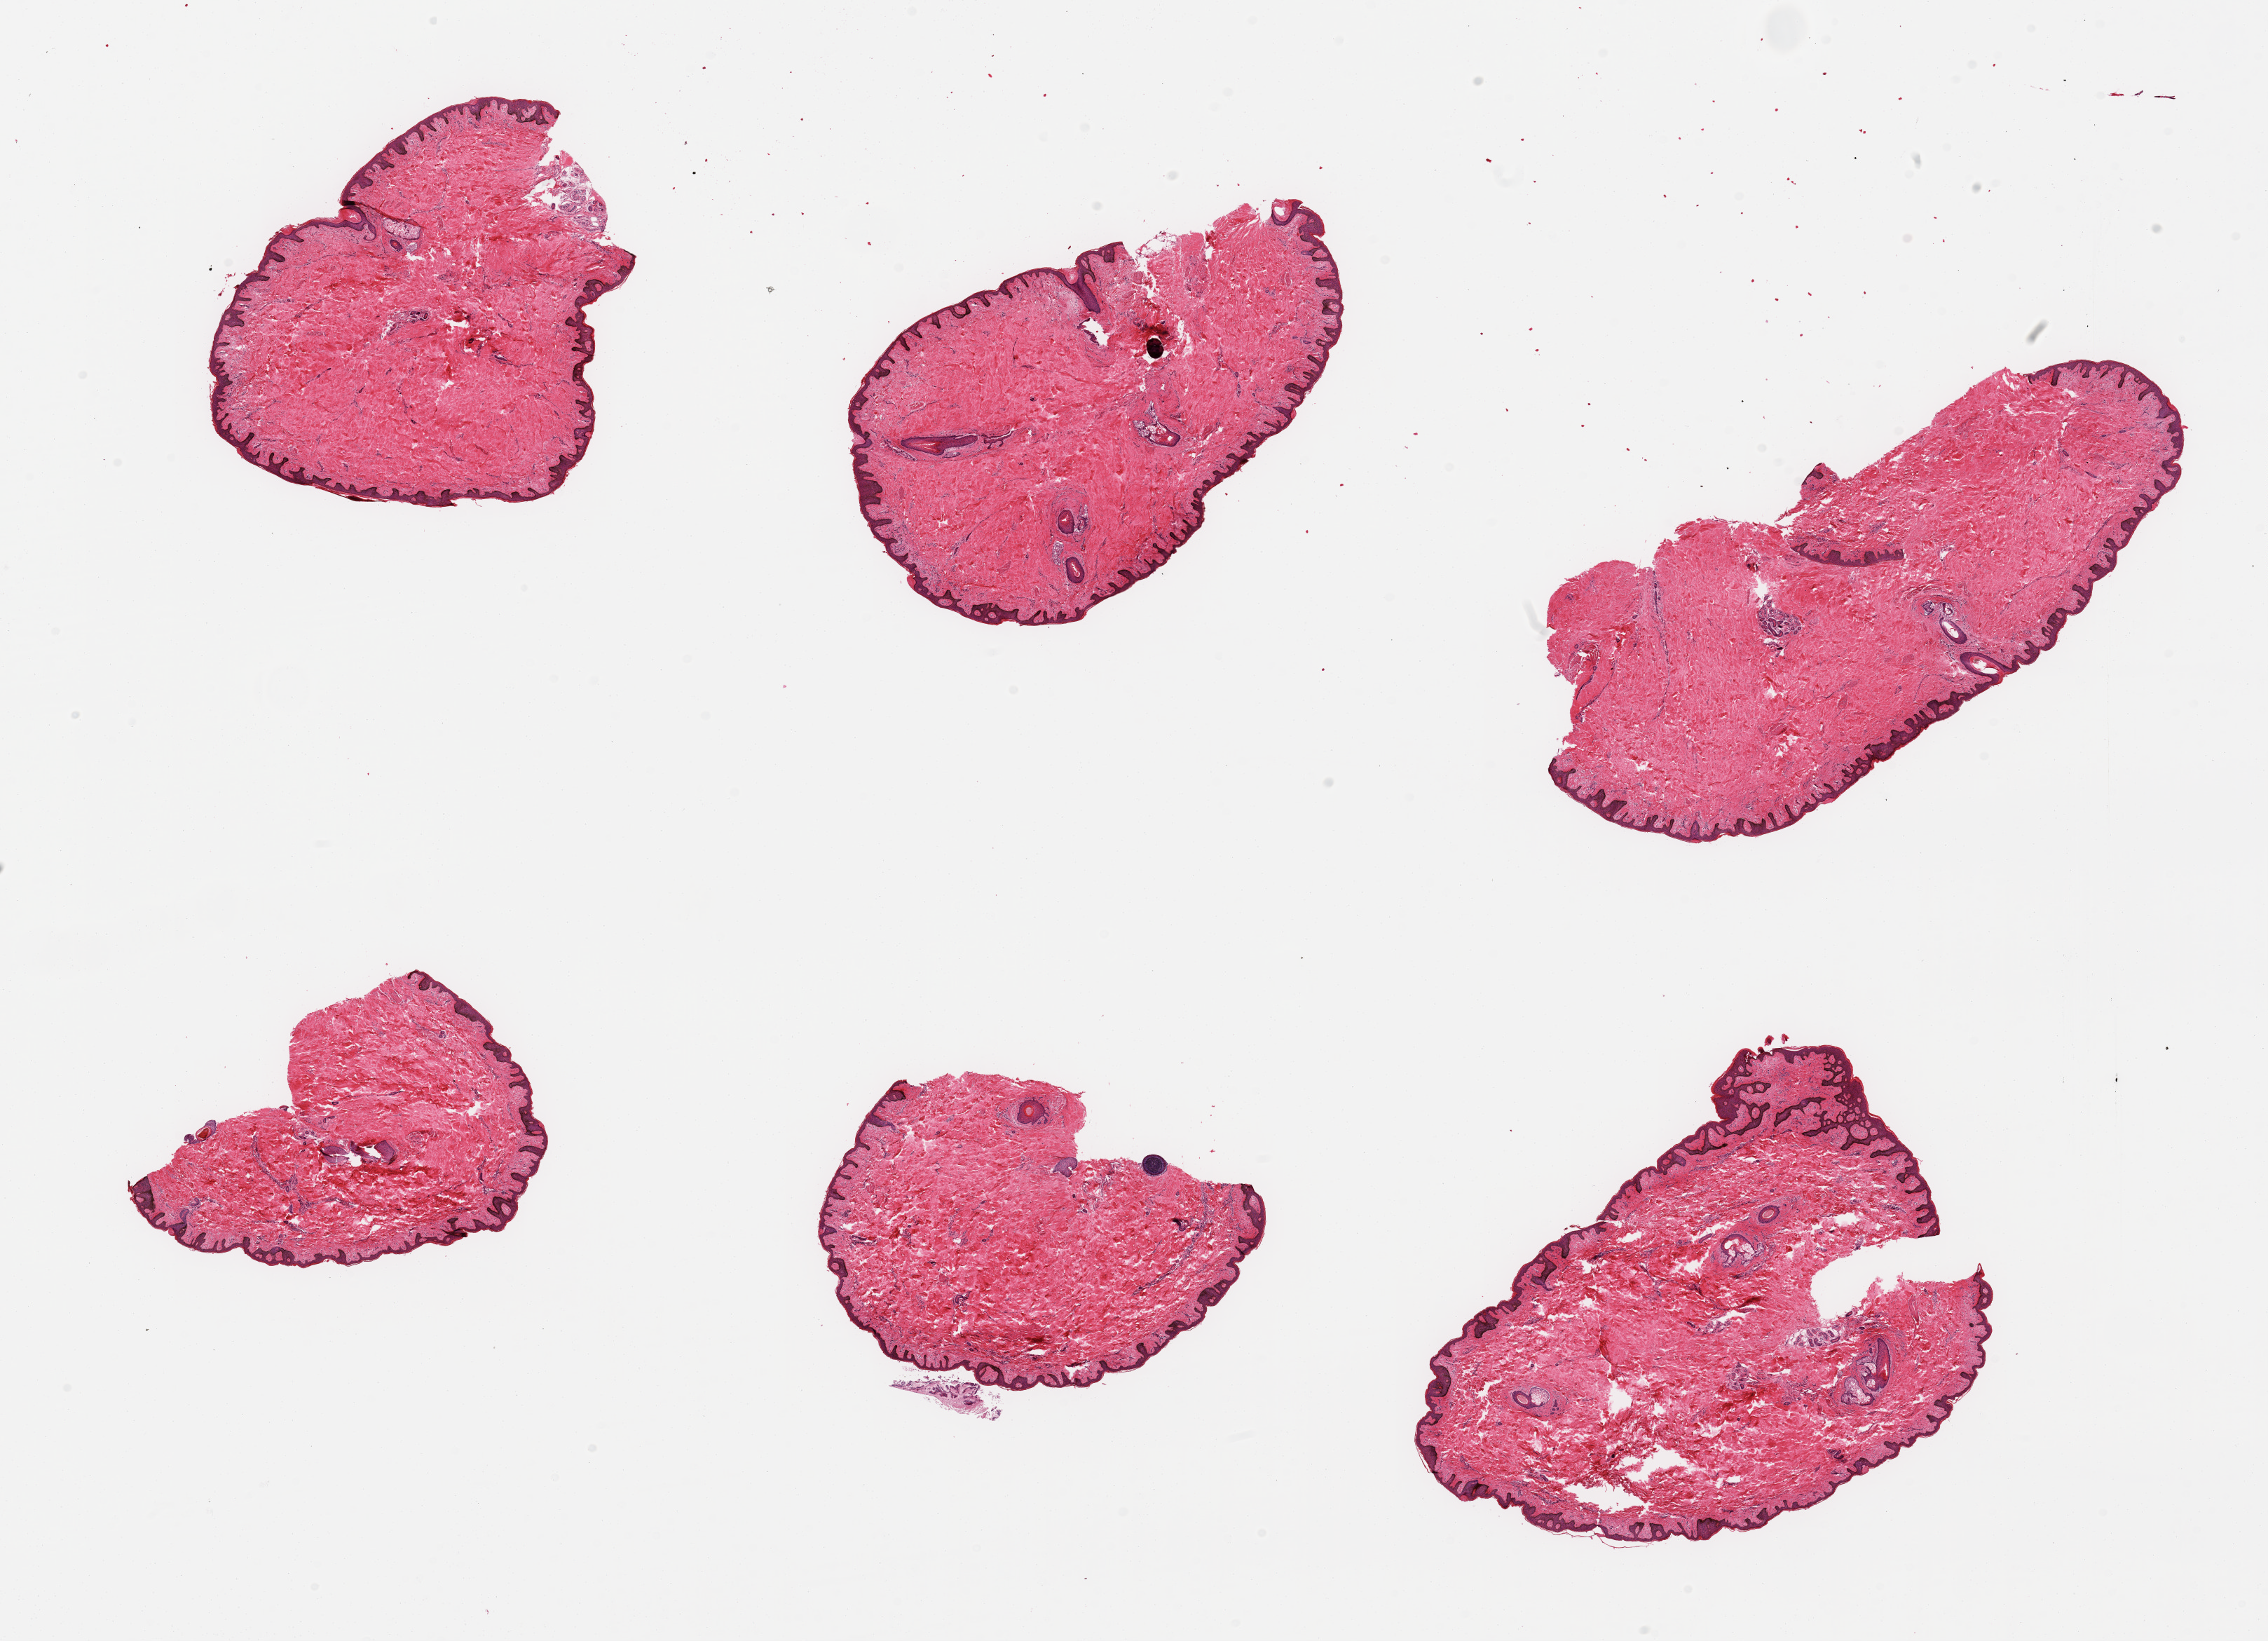
Digitized hematoxylin and eosin (H&E)-stained section — a low-resolution overview of the entire scanned area, about 25.6 x 18.5 mm (slide scanned at 20x); PAXgene-fixed paraffin-embedded (PFPE) section; sampled site (target tissue): skin of suprapubic region; donor tissue sample. Male donor.
Pathologist's review note for this sample: 6 pieces, no dermal fat; squamous epithelium is ~40-50 microns.